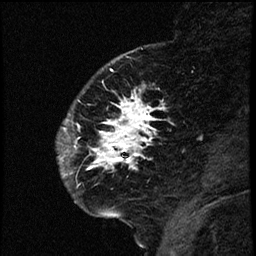
Breast MRI (dynamic contrast-enhanced), one sagittal slice. Slice 17 of 66 in the series (ordered by position). Dynamic contrast-enhanced study with each time point stored as its own series, time point 2 of 3 at this slice position (early post-contrast, ordered by acquisition time). 1.5 T. TE 4.2 ms, TR 17.6 ms. 256 × 256 image matrix, field of view 200 × 200 mm. Female patient. Case-level facts recorded for this patient, not image findings: setting: breast cancer imaged before/during neoadjuvant chemotherapy; receptor status: HER2-positive.
Annotated regions visible in this slice (semi-automatic segmentation, software-assisted and operator-edited):
- analysis volume of interest (the breast-tissue region the enhancement analysis was run in; not a lesion): box from (x=59, y=69) to (x=174, y=209) px
- tumour enhancement mask (voxels above the 100 % enhancement threshold inside the analysis volume of interest): (x=62, y=96)–(x=165, y=176)